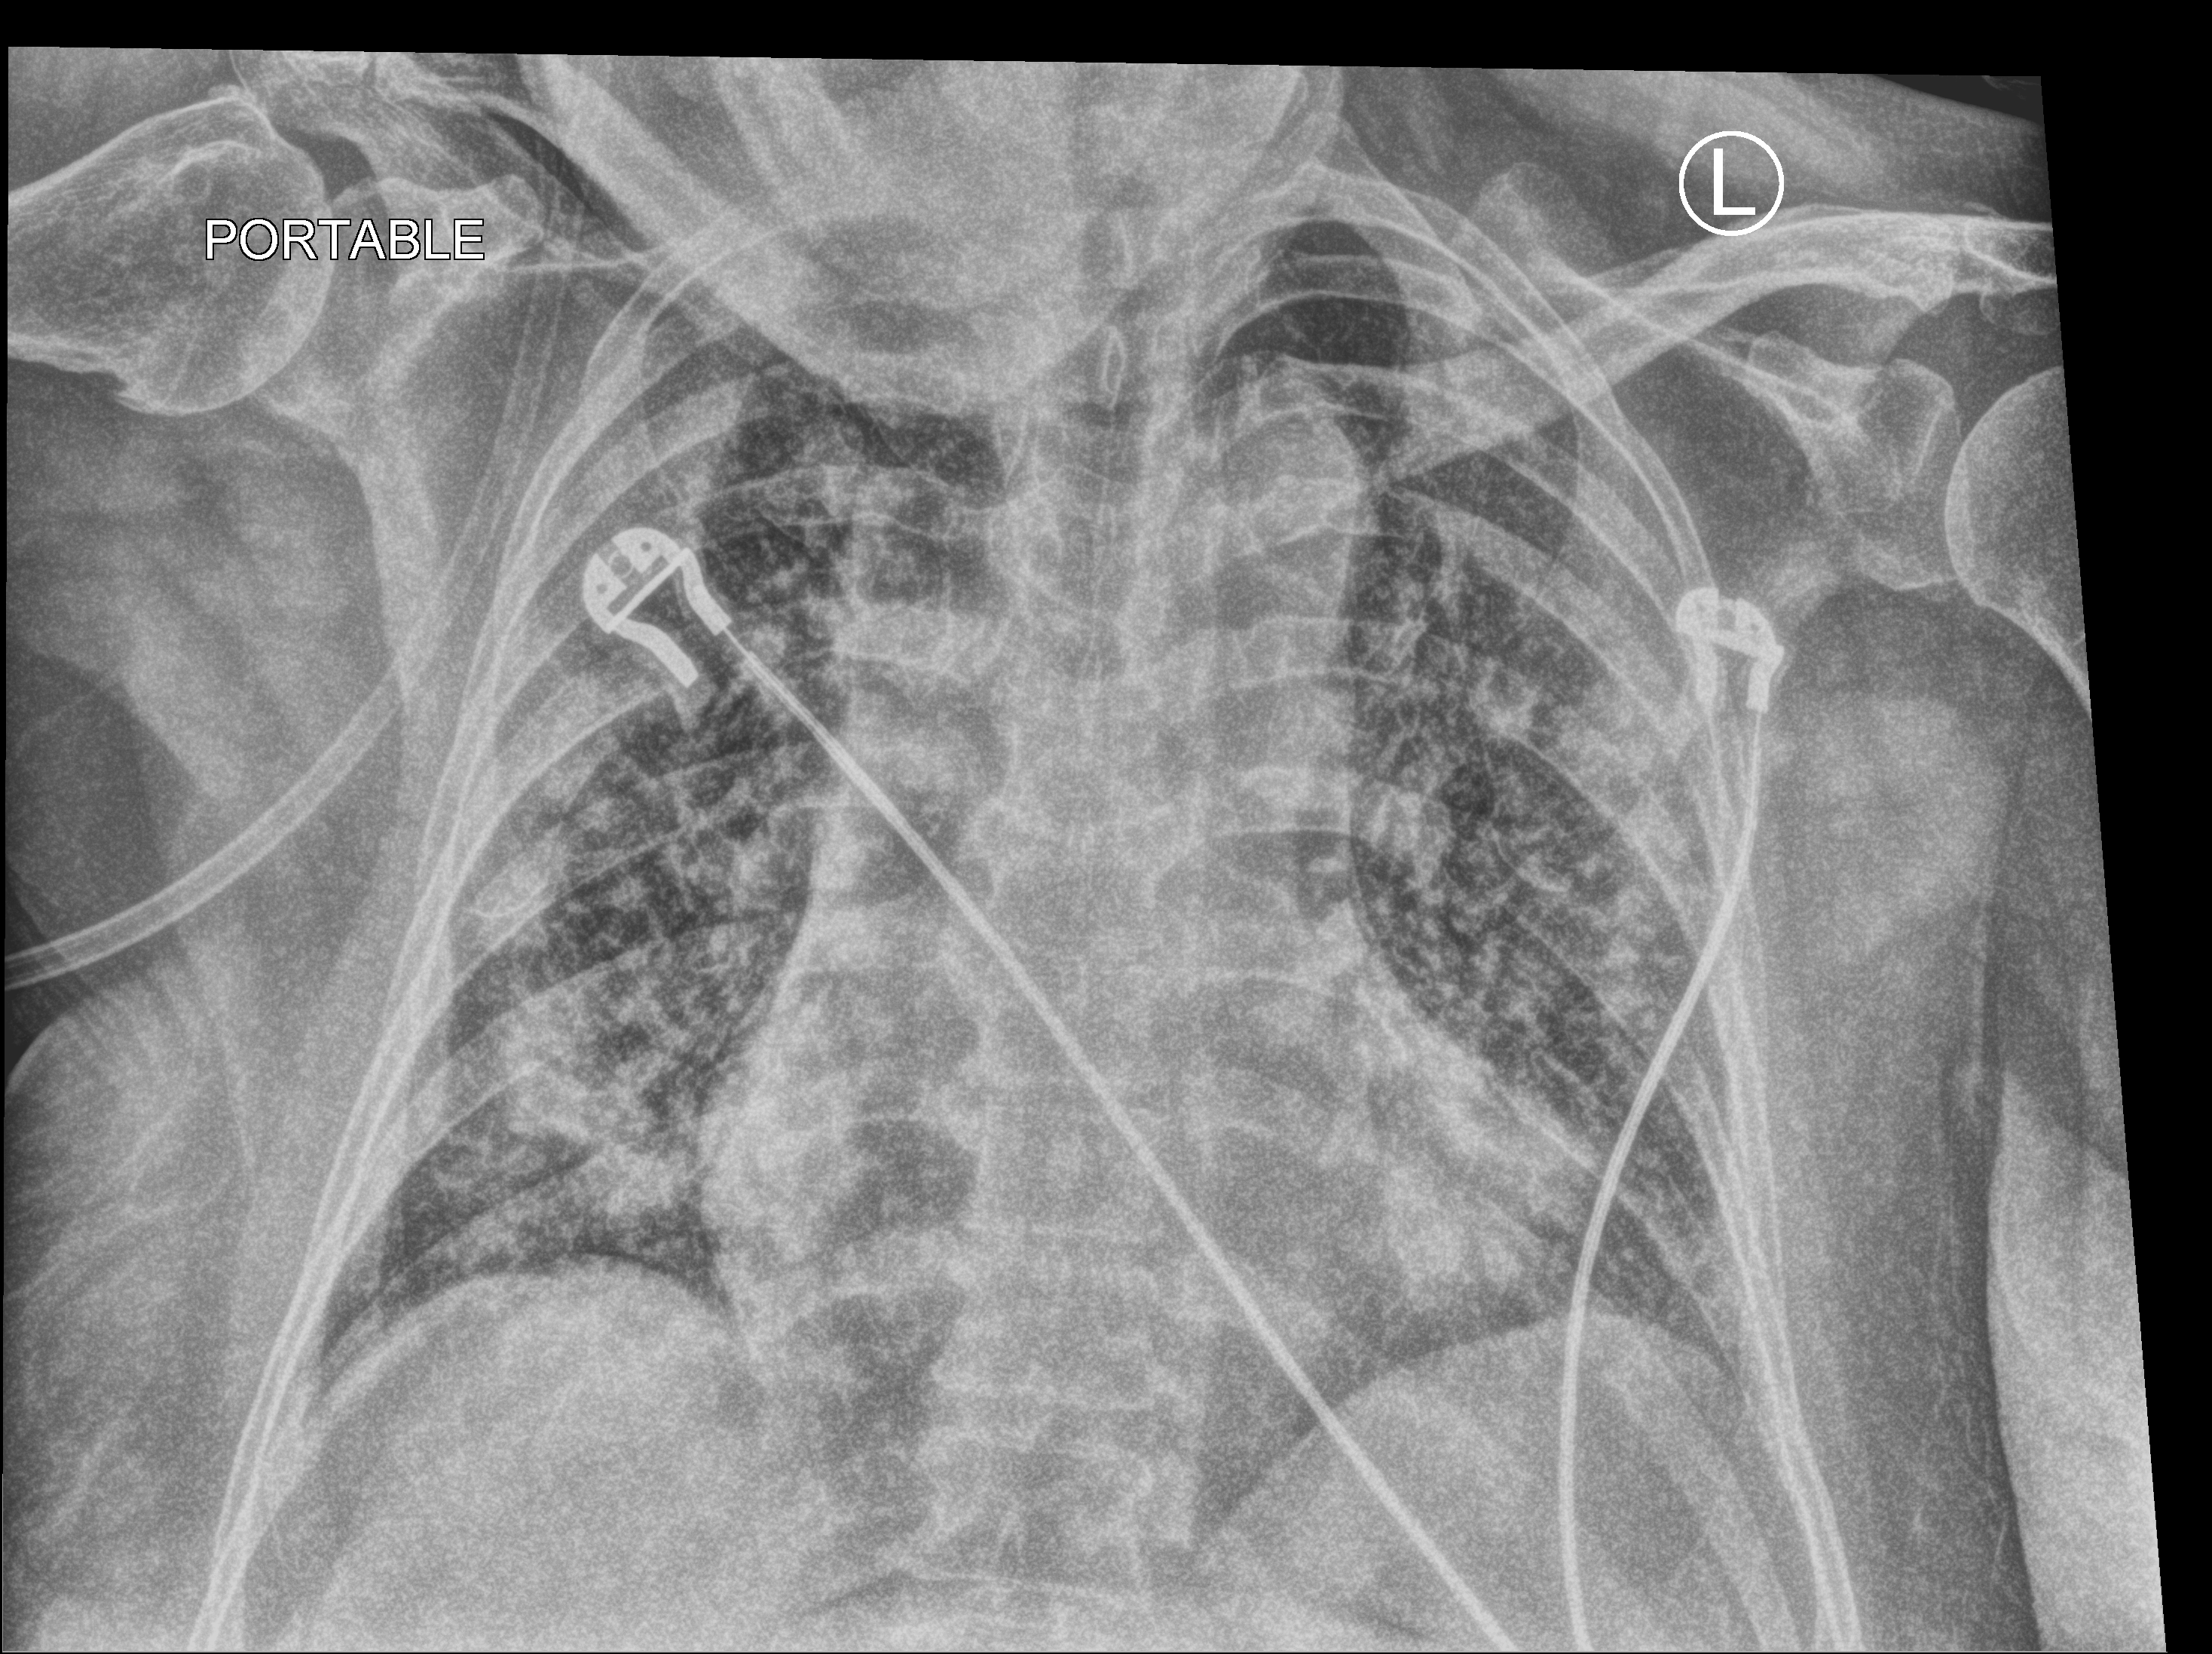
Bedside chest radiograph (computed radiography). Female patient hospitalised with COVID-19, age 60–74 years.
Admission-level facts for this patient (not findings on this image; timing relative to this image not recorded):
- mechanically ventilated during this hospital stay: no